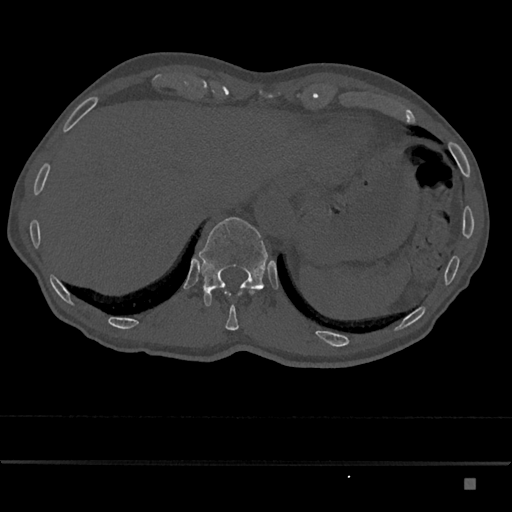
CT including the spine, one axial slice; slice 639 of 797 in the series (ordered by position); 120 kVp; bone window (W 1800 / L 400 HU); 0.5 mm slice thickness; 512 × 512 image matrix. Patient: male, 72 years. Case-level facts recorded for this patient, not image findings: primary cancer: prostate.
Outlined on this slice (semi-automatically segmented with operator editing):
- T11 vertebra: box from (x=225, y=291) to (x=254, y=330) px
- T12 vertebra: (x=199, y=217)–(x=268, y=306)